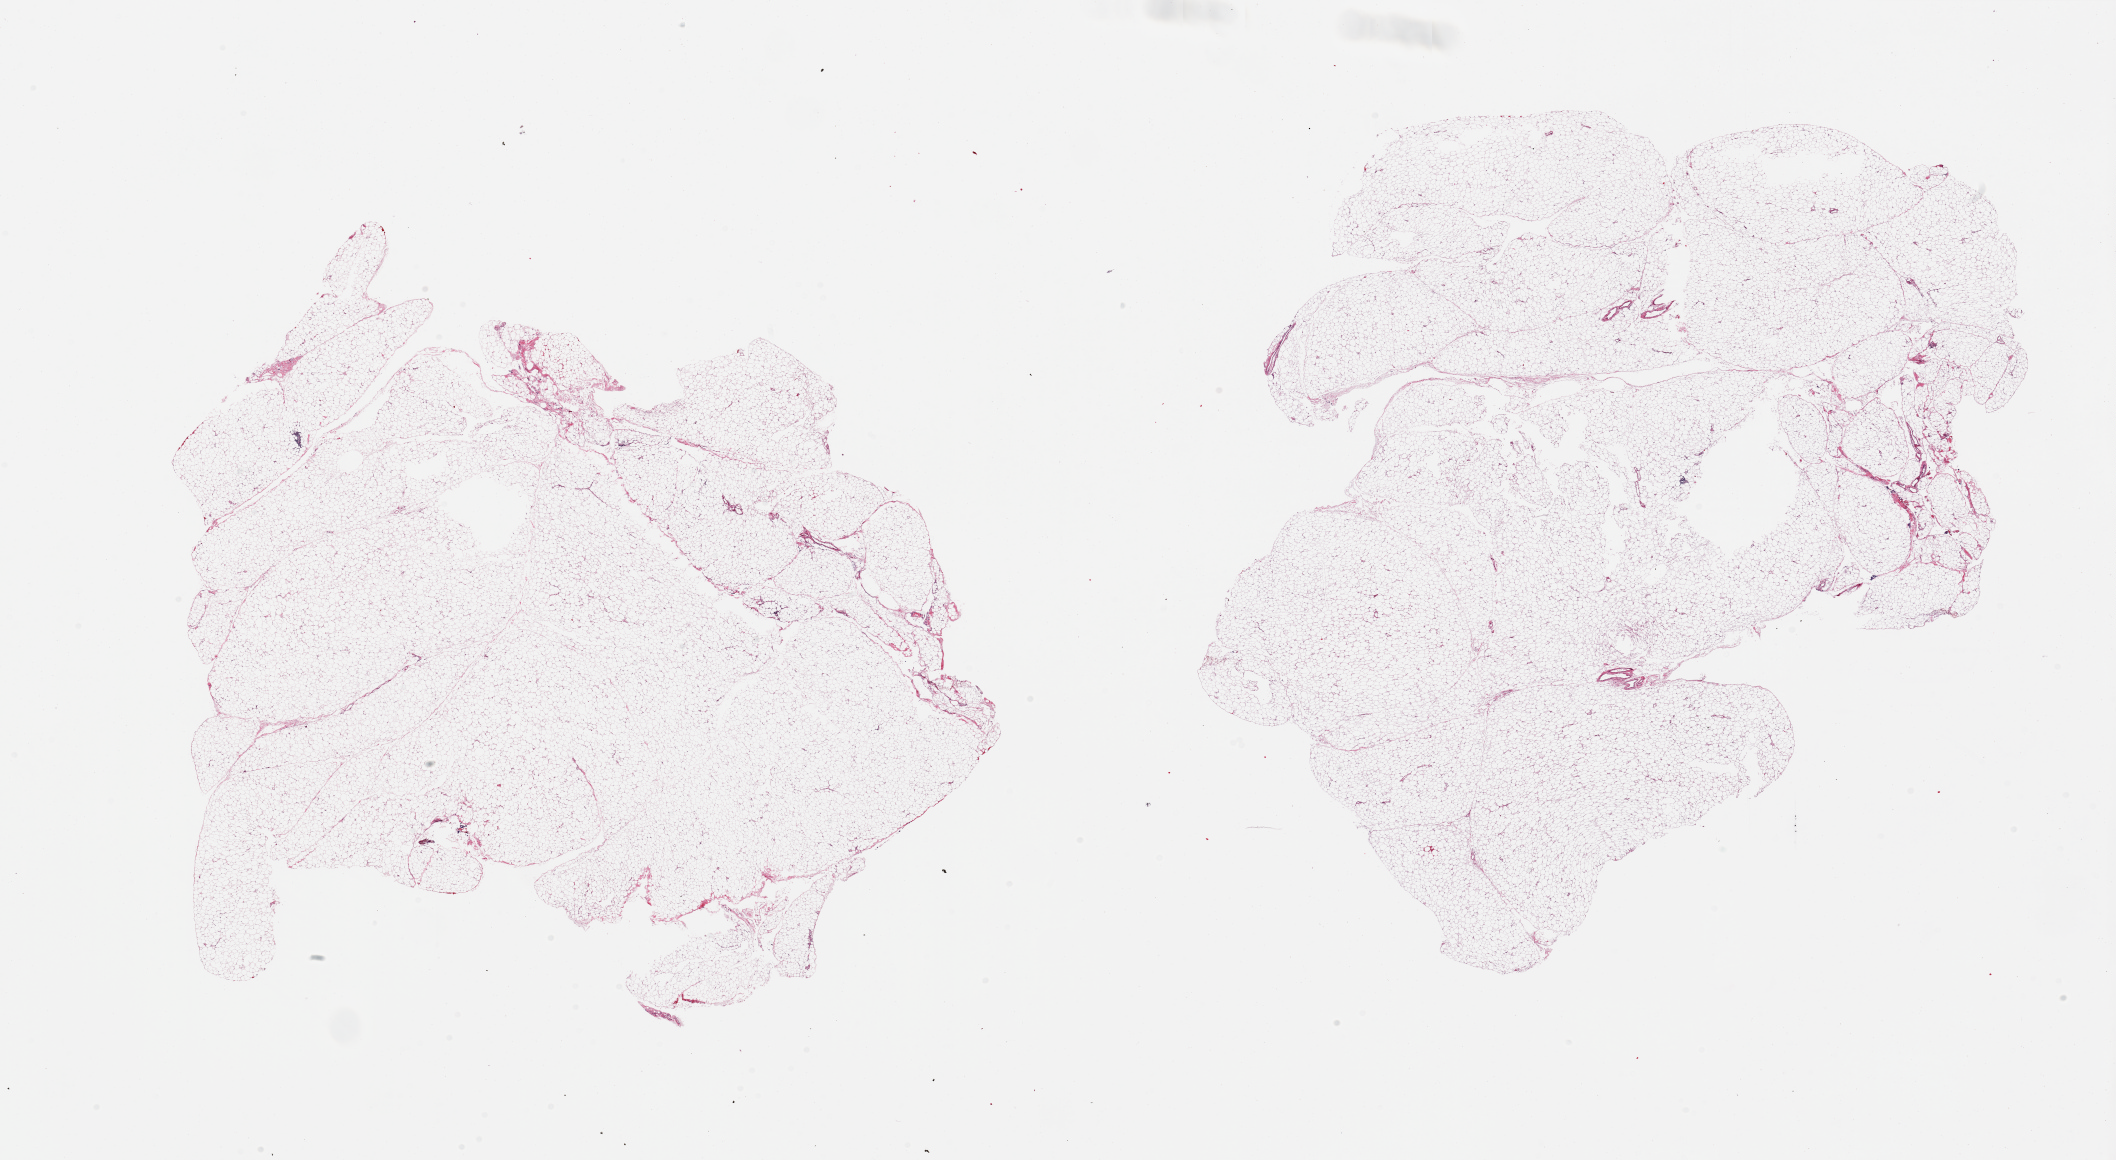
Whole-slide image, H&E stain, brightfield, a low-resolution overview of the entire scanned area, about 33.5 x 18.3 mm. PAXgene-fixed, paraffin-embedded tissue. Sampled site (target tissue): omentum. Tissue donor sample. Female donor.
Review note (as recorded): 2 pieces, essentially pure adipose tissue.